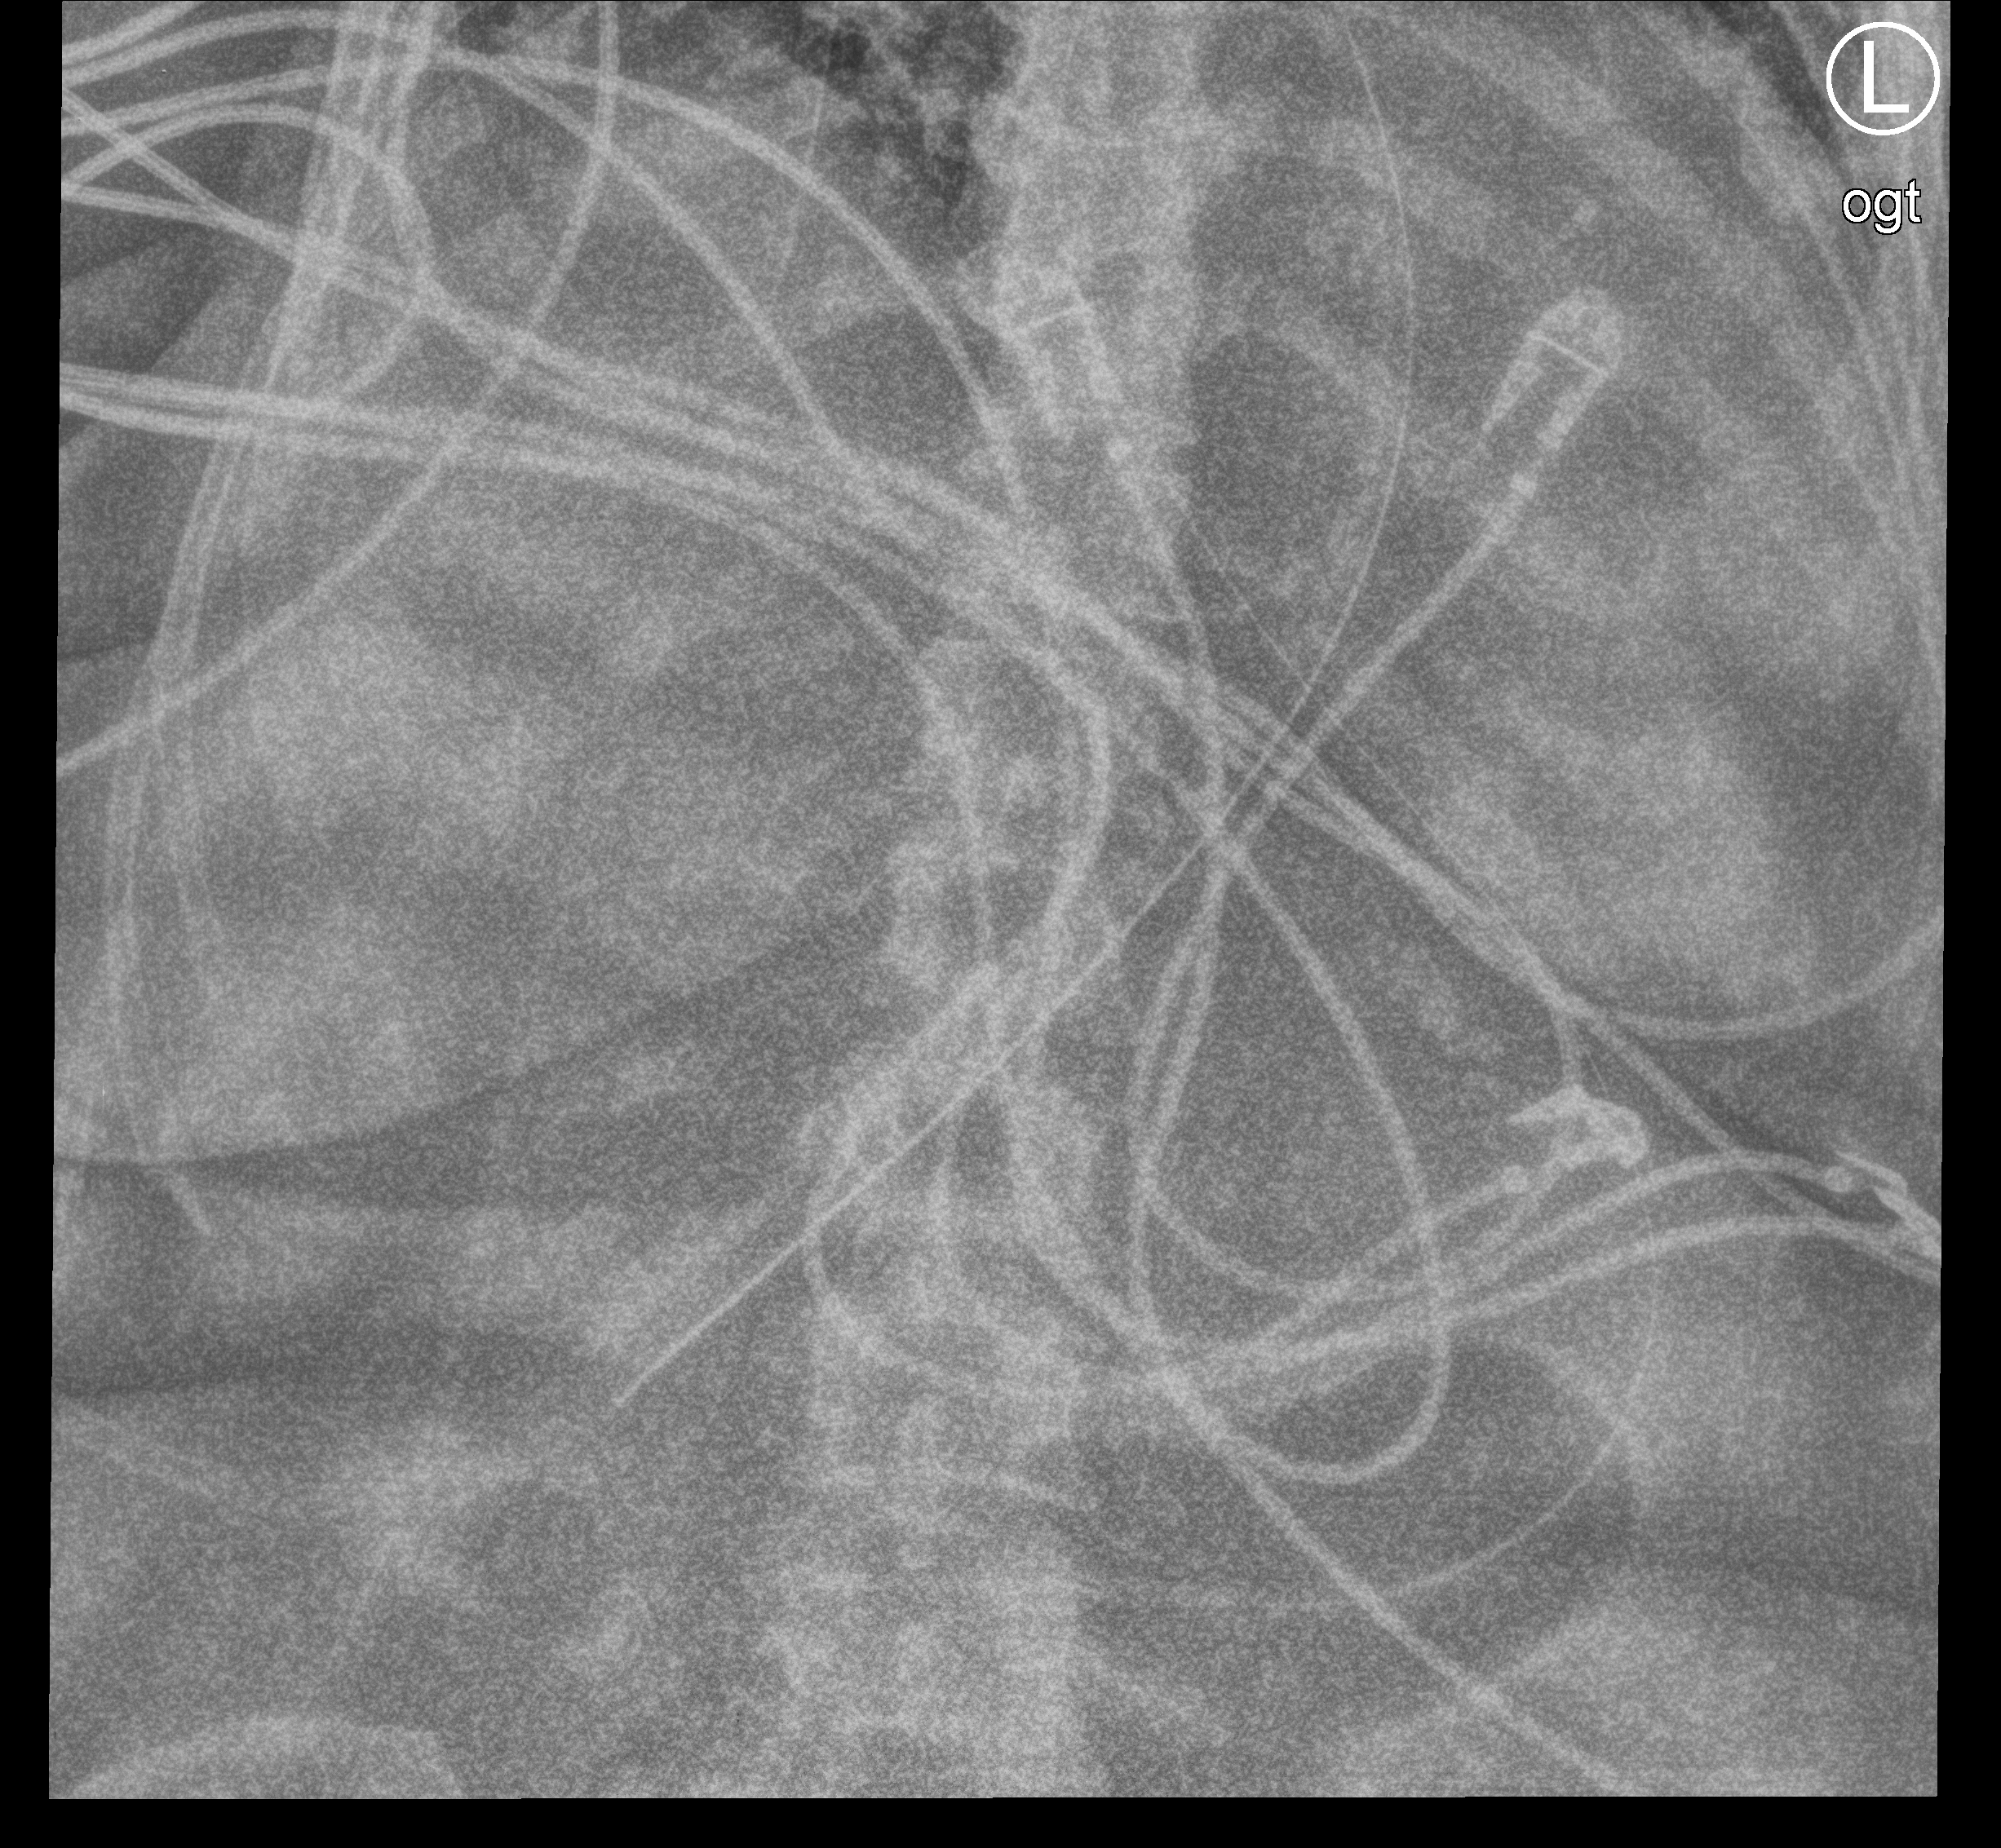
Bedside chest radiograph (computed radiography), anteroposterior (AP) projection. Female patient hospitalised with COVID-19, age 60–74 years.
Admission-level facts for this patient (not findings on this image; timing relative to this image not recorded): admitted to intensive care during this hospital stay: yes.